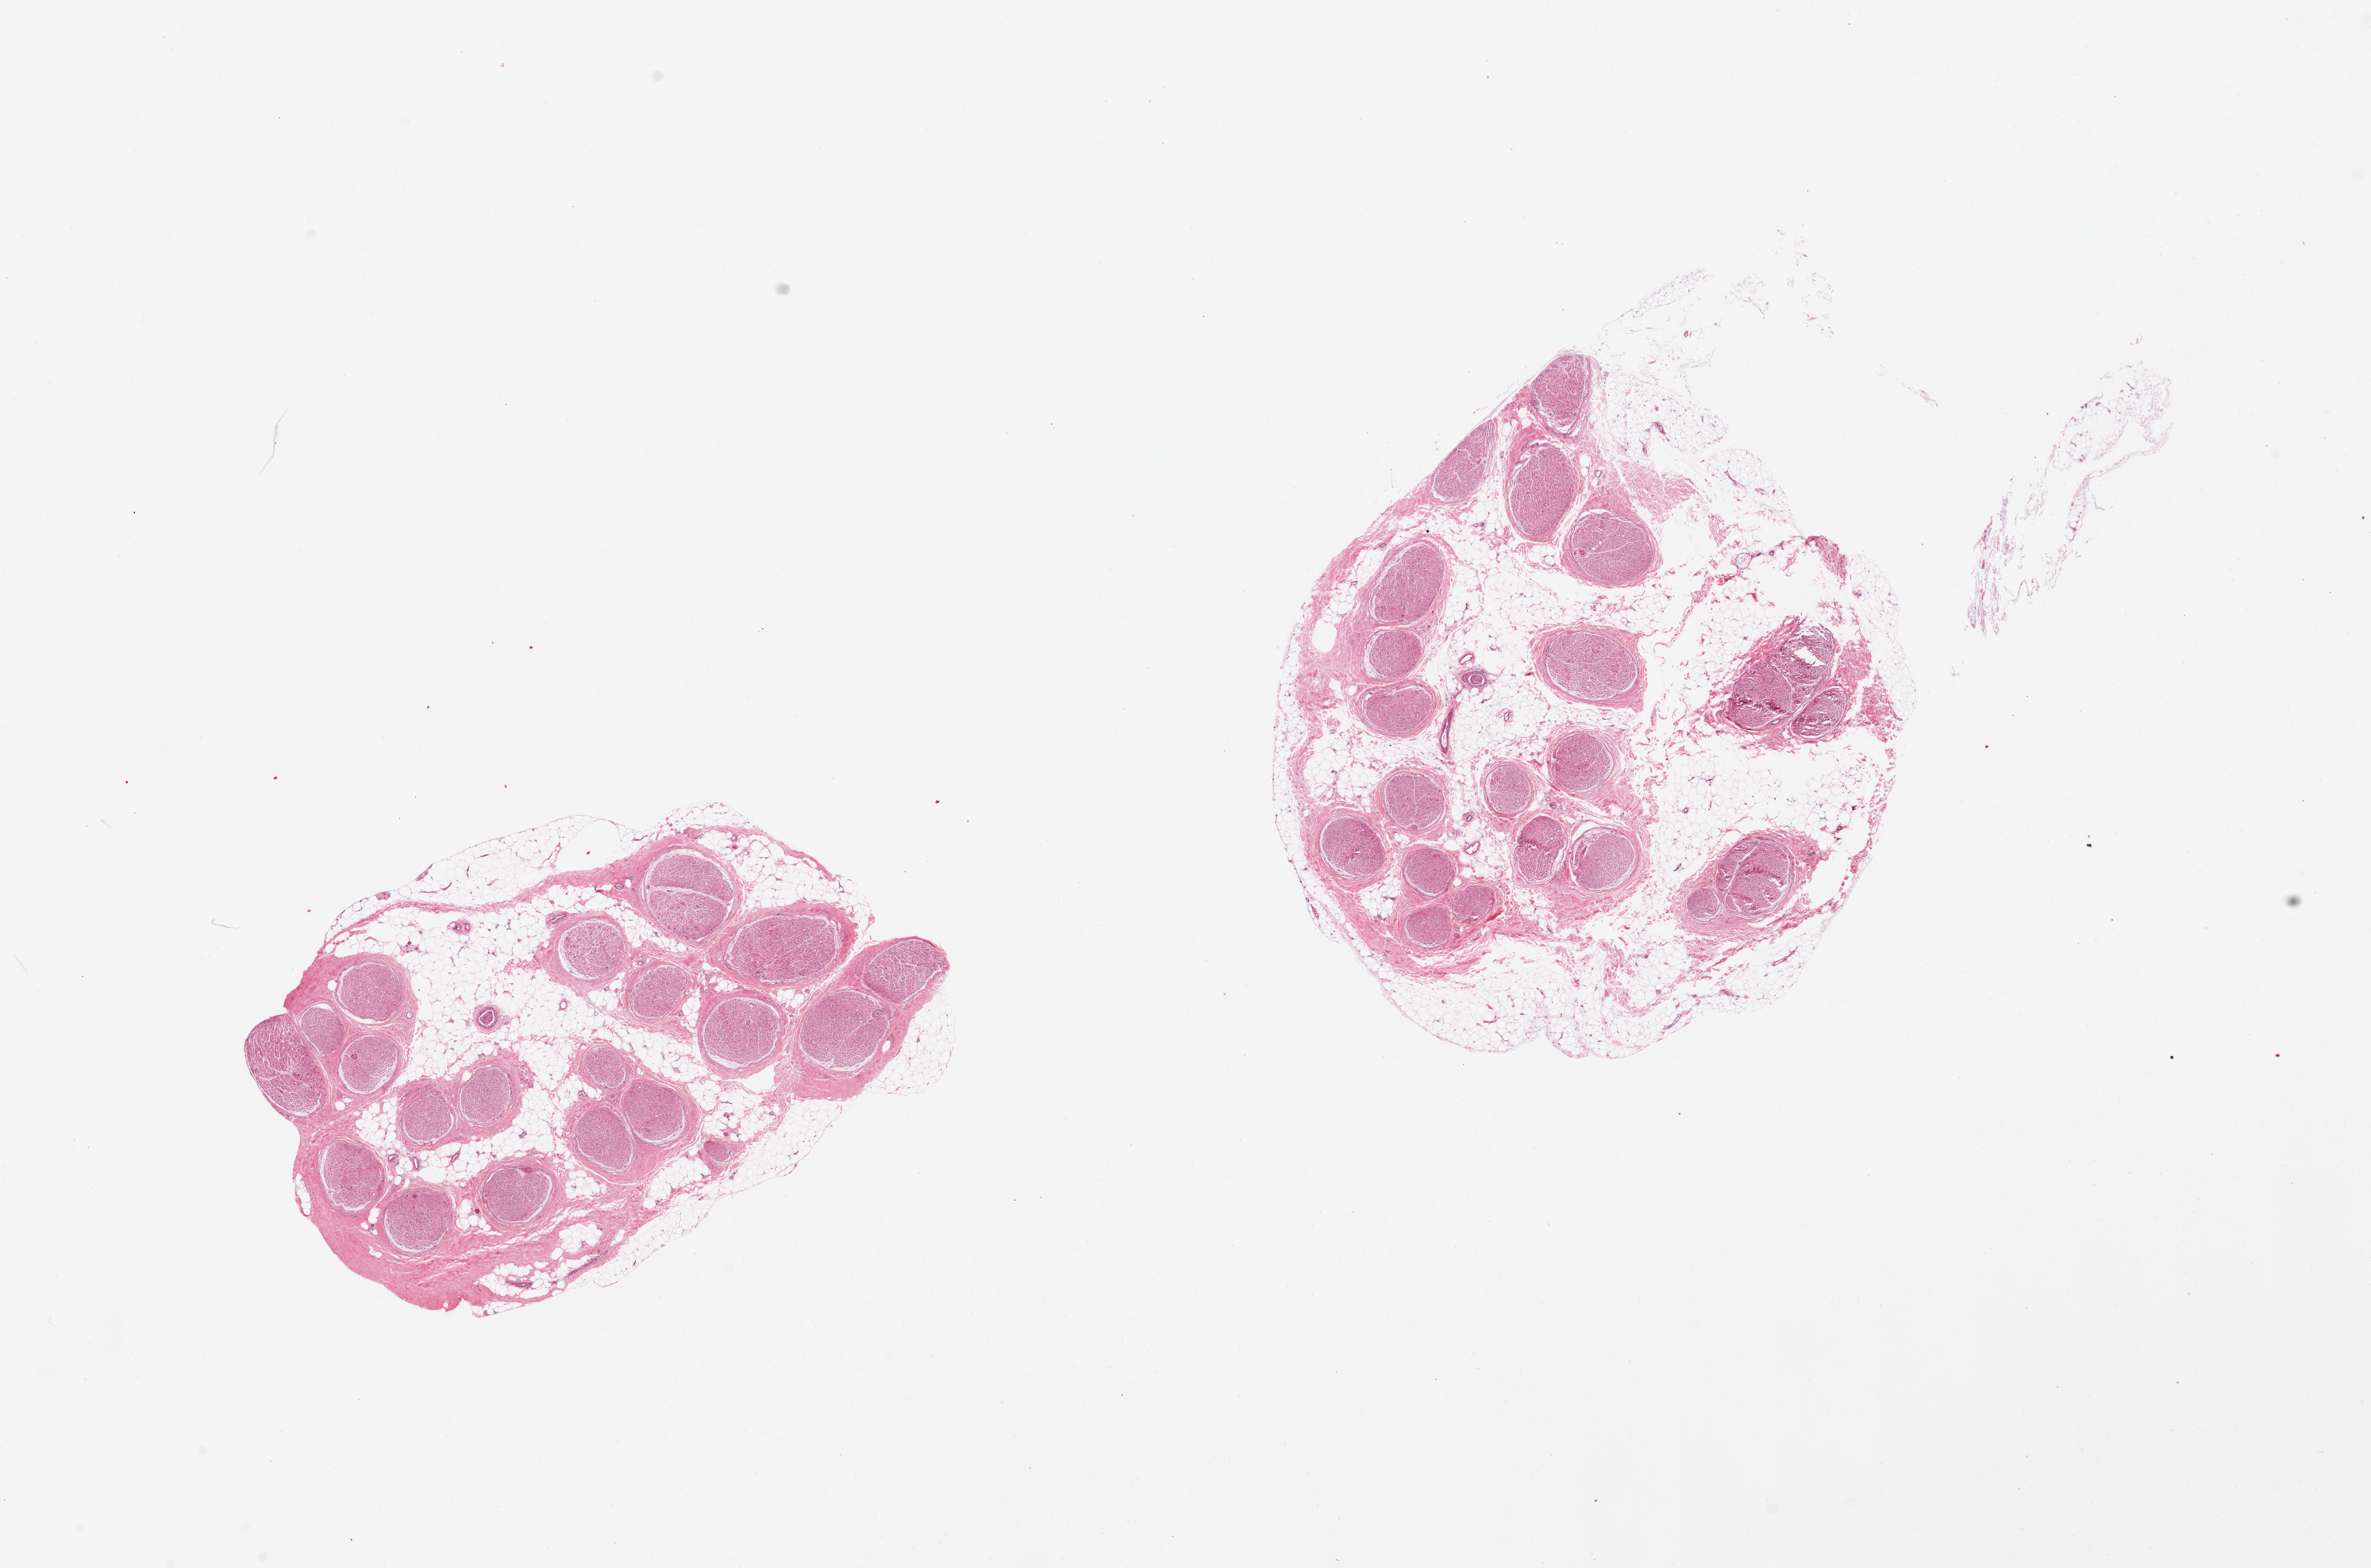
Digitized hematoxylin and eosin (H&E)-stained section, low-resolution overview of the scanned area, about 23.6 x 15.6 mm (acquisition: 20x scan). PAXgene-fixed, paraffin-embedded tissue. Sampled site (target tissue): tibial nerve. Donor tissue sample.
Pathologist's review note for this sample: 2 pieces, 50-60% is internal and attached fat.